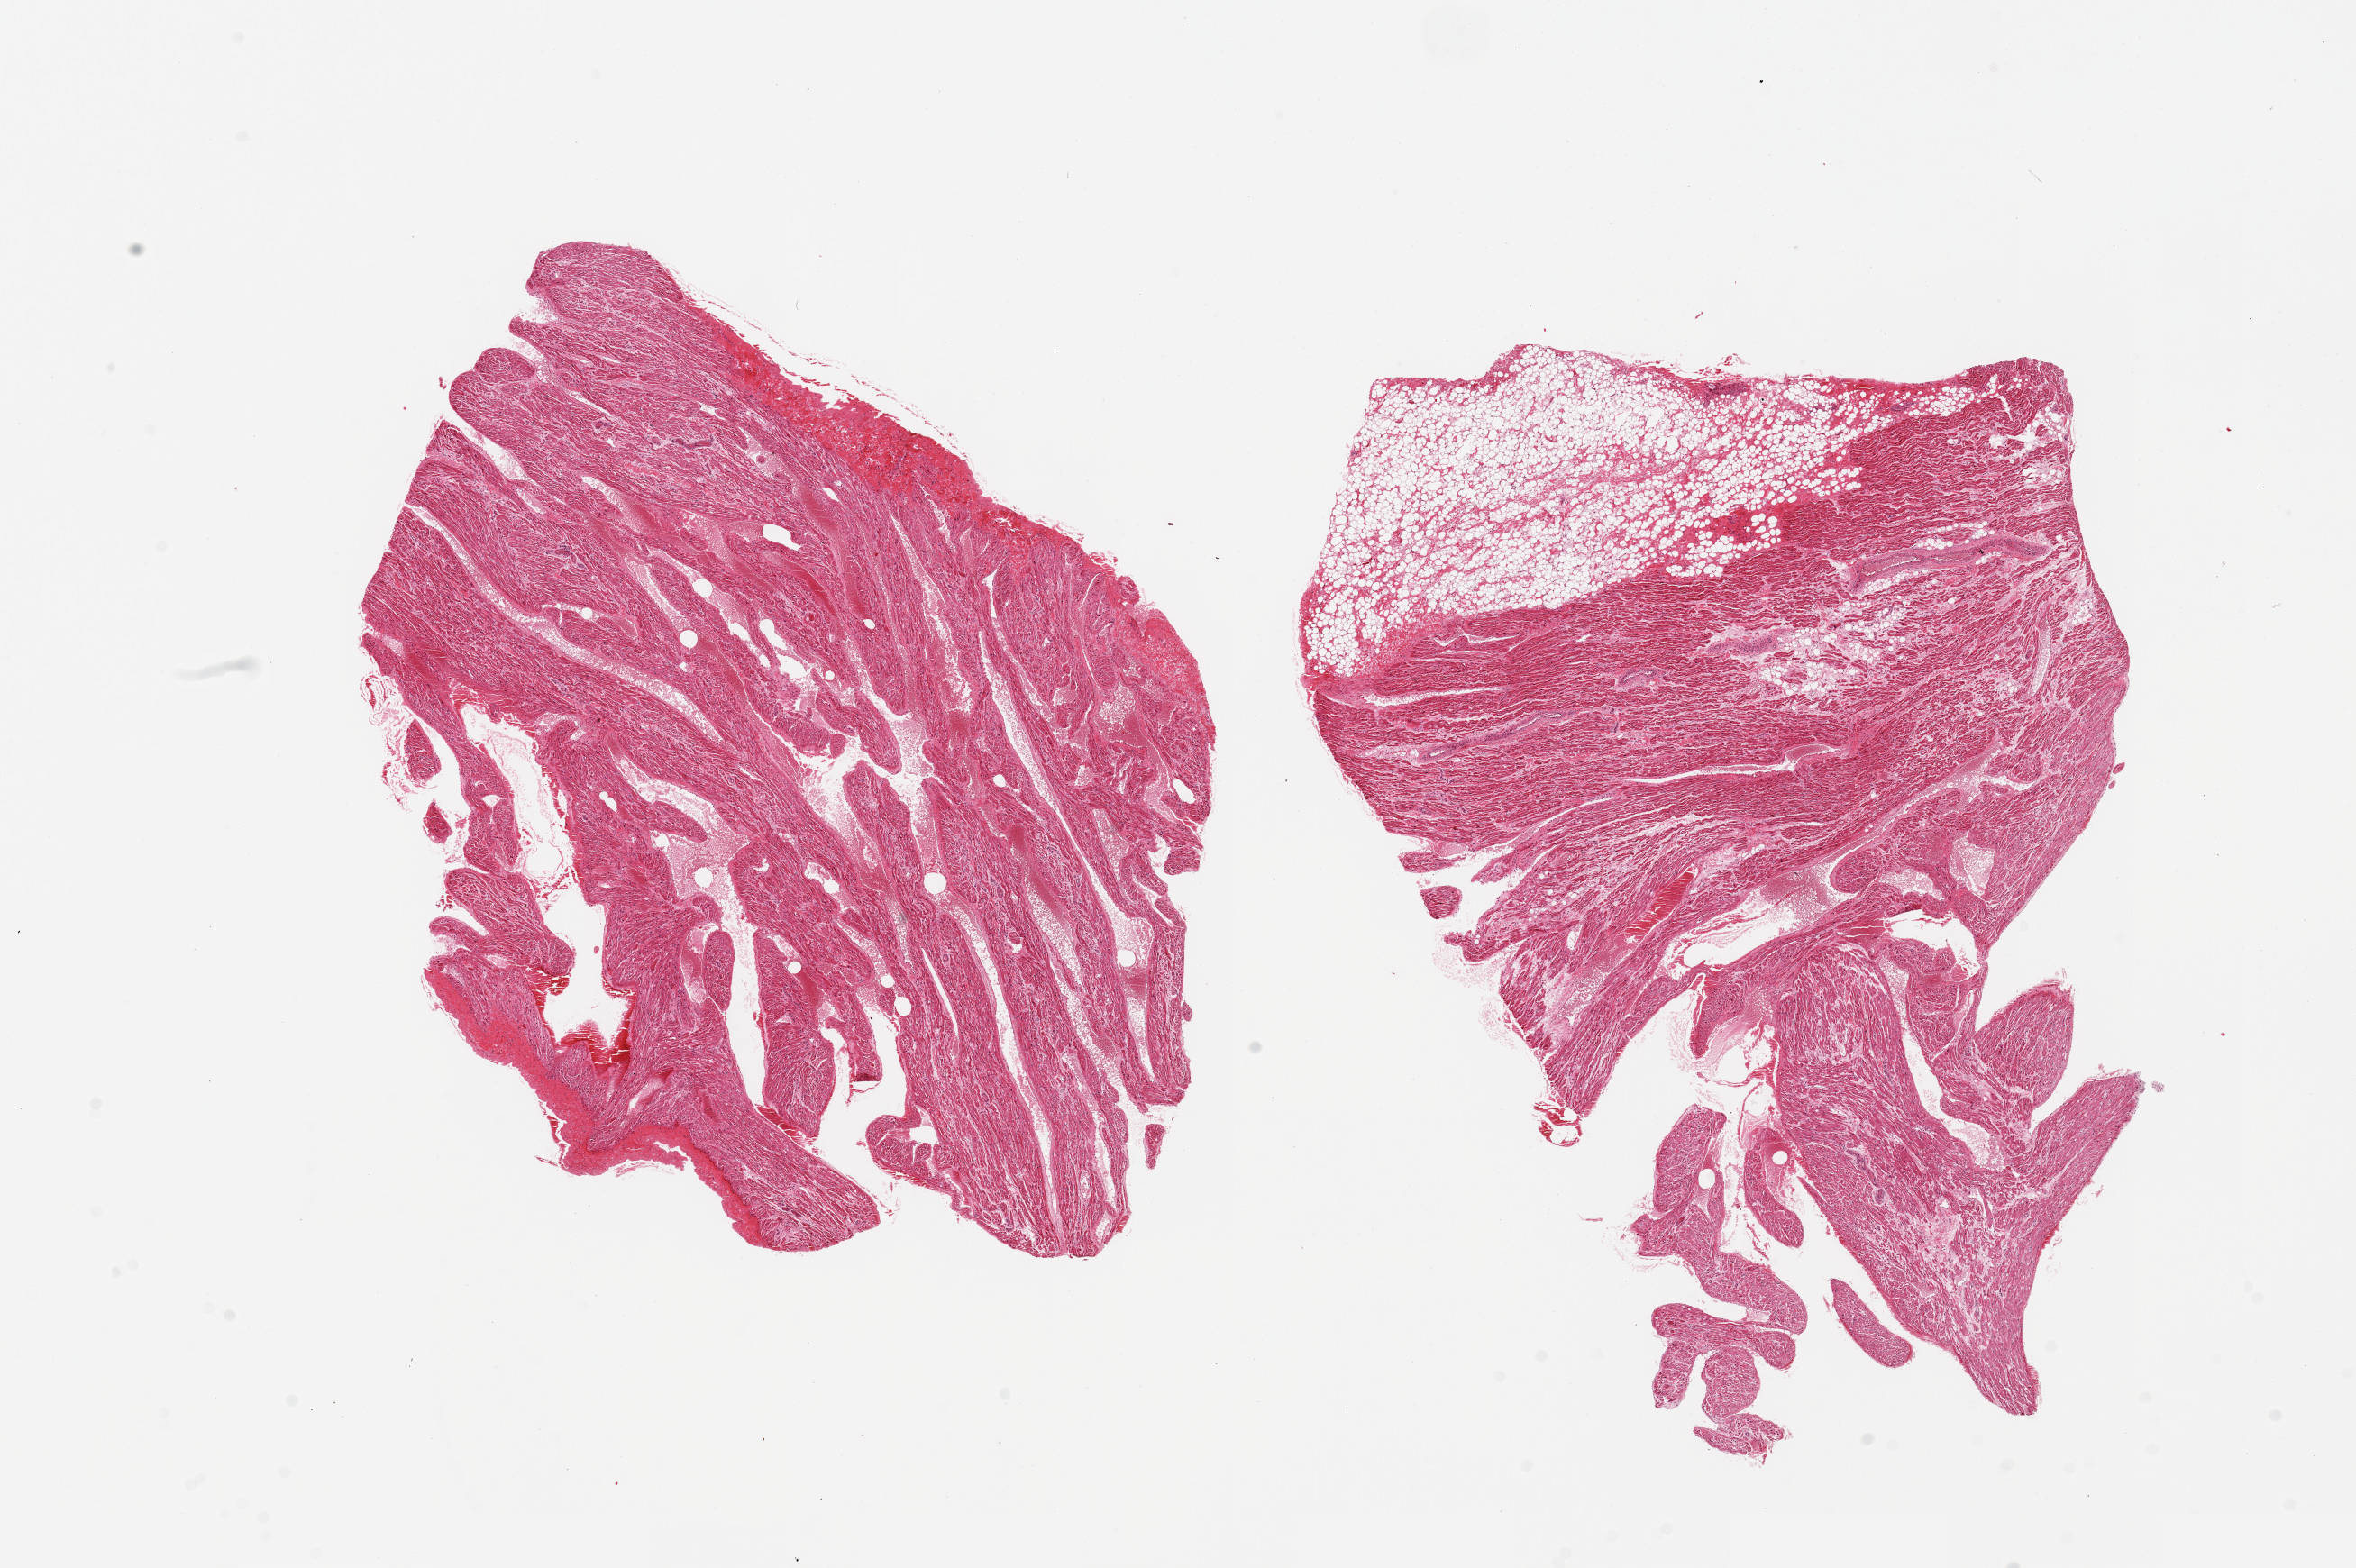
Haematoxylin and eosin whole-slide image — shown as a low-resolution overview of the whole scanned area (about 20.7 x 13.8 mm); PAXgene-fixed, paraffin-embedded tissue; sampled site (target tissue): auricular appendage; tissue donor sample. Male donor.
Reviewer comment on this tissue sample: 2 pieces, 10x7 & 11x7.5mm.